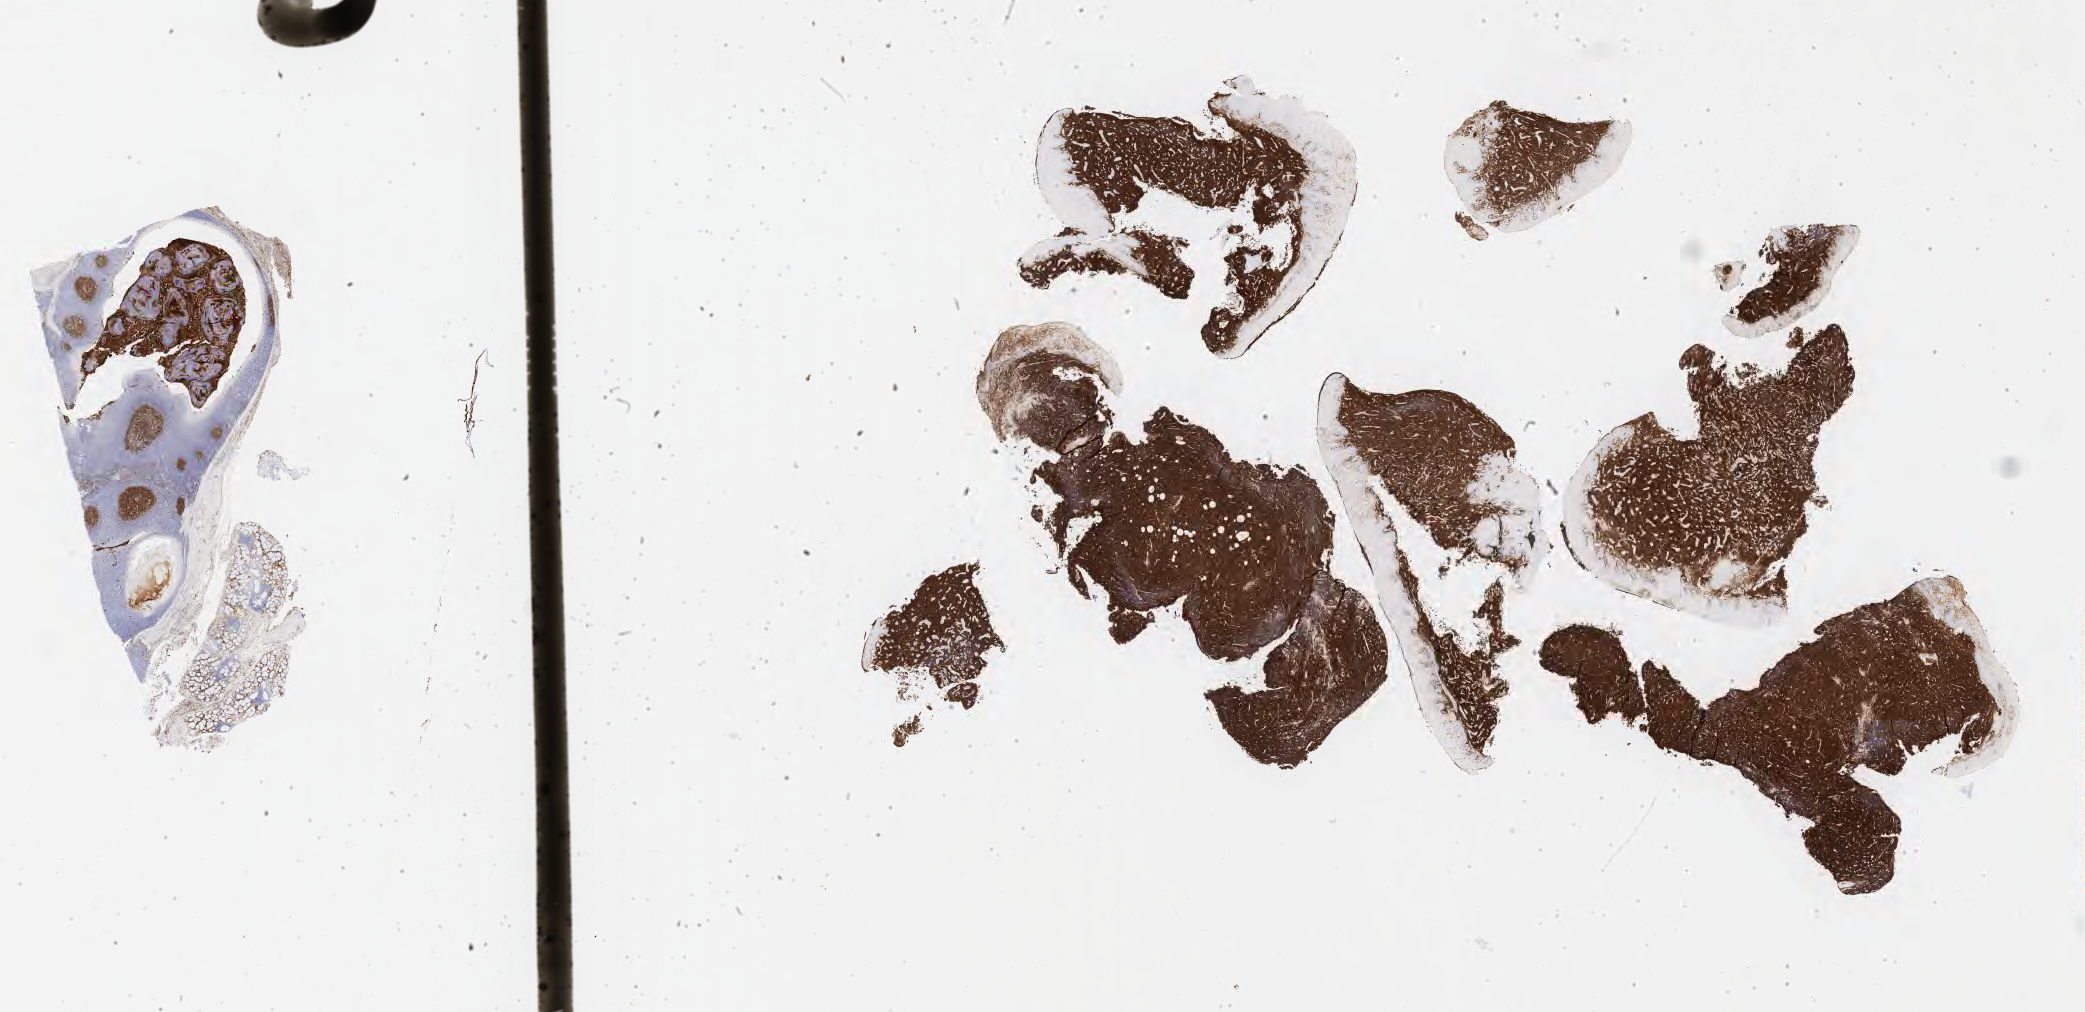
IHC for CD10, whole-slide image, whole scanned area (about 33.7 x 16.4 mm) shown as a low-resolution overview. Tumor tissue. Patient: male, aged 43.
Diagnosis: Burkitt lymphoma, NOS.